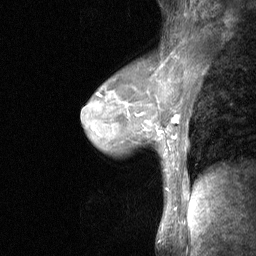
Breast MRI (dynamic contrast-enhanced), one sagittal slice. Position 40 of 64 along the scan axis. Dynamic contrast-enhanced study with each time point stored as its own series, time point 2 of 3 at this slice position (early post-contrast, ordered by acquisition time). 1.5 T. TE 4.8 ms, TR 27 ms. 2 mm slice thickness. 256 × 256 image matrix, field of view 200 × 200 mm. Patient: female, 44 years. From the clinical record (not read from this slice): setting: breast cancer imaged before/during neoadjuvant chemotherapy; receptor status: HR-positive, HER2-negative.
Annotated regions visible in this slice (semi-automatic segmentation, software-assisted and operator-edited):
- analysis volume of interest (the breast-tissue region the enhancement analysis was run in; not a lesion): bounding box (x1, y1, x2, y2) in pixels: (140, 109, 180, 148)
- tumour enhancement mask (voxels above the 90 % enhancement threshold inside the analysis volume of interest): (158, 115, 179, 138)